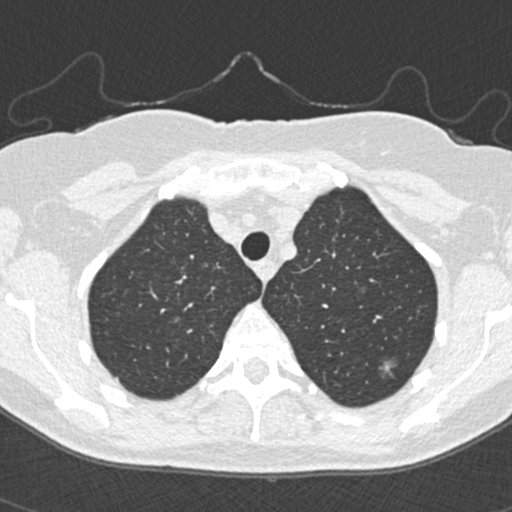
Low-dose screening chest CT, one axial slice. Slice 298 of 350 in the series (ordered by position). Reconstruction kernel B30f. 120 kVp. Lung window (W 1500 / L -600 HU). 1 mm slice thickness. 512 × 512 image matrix.
Structures marked on this image (outlined manually by an expert reader):
- lesion 2 (tumor, upper lobe of left lung): box from (x=380, y=360) to (x=394, y=374) px